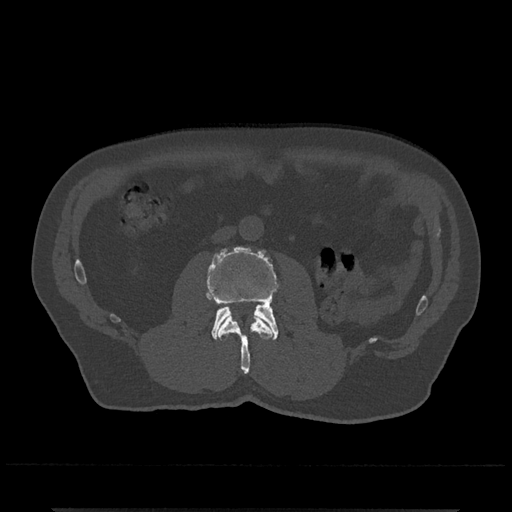
CT including the spine, one axial slice. Slice 251 of 797 in the series (ordered by position). Reconstruction kernel Br40s/3. 120 kVp. Bone window (W 1800 / L 400 HU). 0.5 mm slice thickness. 512 × 512 image matrix. Patient: male, 67 years. From the clinical record (not read from this slice): primary cancer: prostate.
Structures marked on this image (semi-automatically segmented with operator editing):
- L2 vertebra: box from (x=217, y=314) to (x=273, y=374) px
- L3 vertebra: (x=206, y=246)–(x=278, y=340)